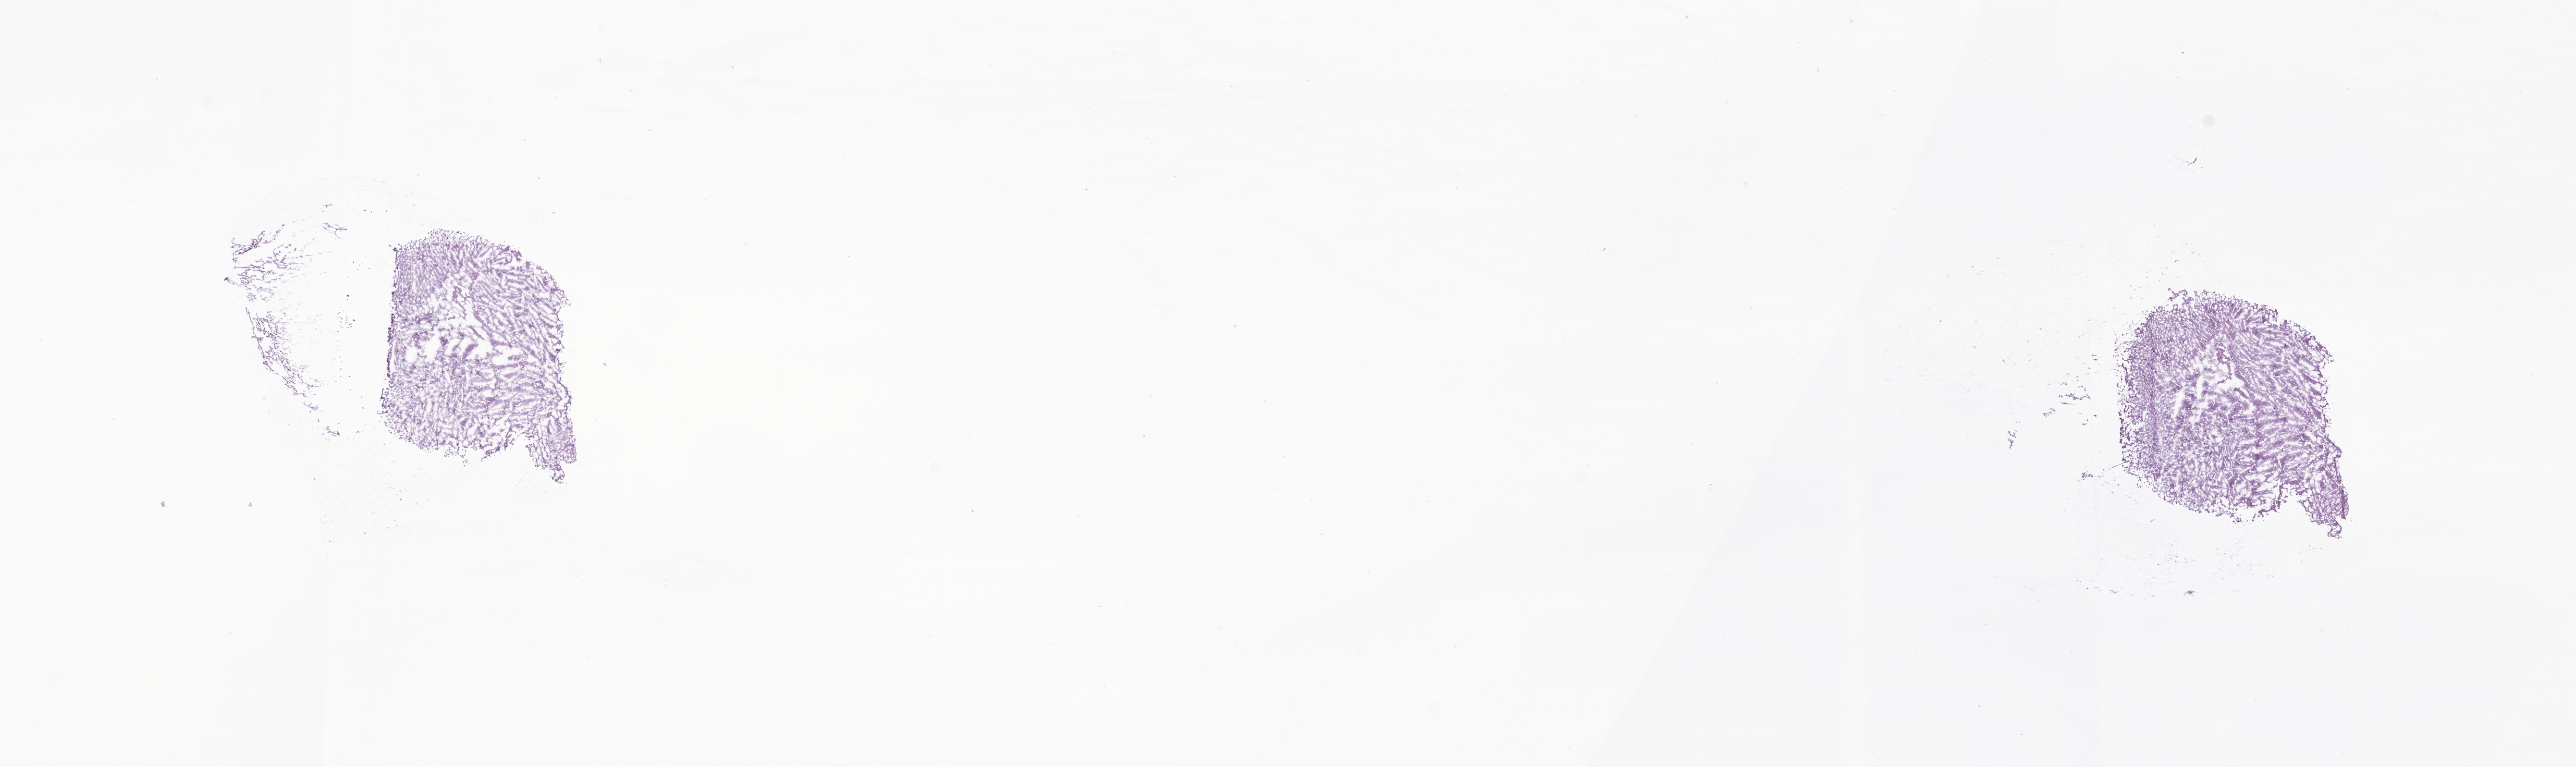
Digitized hematoxylin and eosin (H&E)-stained section of tumor tissue from the frontal lobe, shown as a low-resolution overview of the whole scanned area (about 20.8 x 6.2 mm), frozen section. Patient: female, age 221 months (18 years 5 months).
Diagnosis: Glioma, malignant.